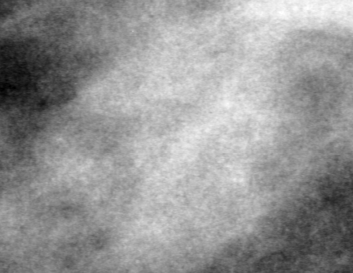
Region of interest cut from a scanned film mammogram (one marked finding); left breast; MLO view; BI-RADS breast density category 4 (scale 1–4).
Finding: calcifications, morphology pleomorphic, distribution clustered; BI-RADS assessment category 4; subtlety rating 2 on a 1 (subtle) to 5 (obvious) scale; pathology result (as recorded, not read from the image): benign.